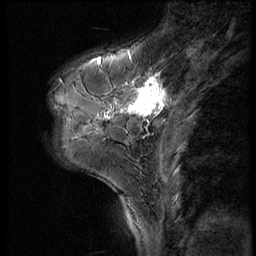
Breast MRI (dynamic contrast-enhanced), one sagittal slice. Slice 18 of 56 in the series (ordered by position). 3 images stored at this slice position (order not interpretable as contrast timing). 1.5 T. TE 4.2 ms, TR 9 ms. 2.5 mm slice thickness. 256 × 256 image matrix. Female patient, age 46 years. Case-level facts recorded for this patient, not image findings: setting: breast cancer imaged before/during neoadjuvant chemotherapy; receptor status: HER2-positive.
Structures marked on this image (semi-automatic segmentation, software-assisted and operator-edited):
- analysis volume of interest (the breast-tissue region the enhancement analysis was run in; not a lesion): bounding box [x1, y1, x2, y2] px = [79, 68, 190, 143]
- tumour enhancement mask (voxels above the 140 % enhancement threshold inside the analysis volume of interest): [105, 74, 167, 120]